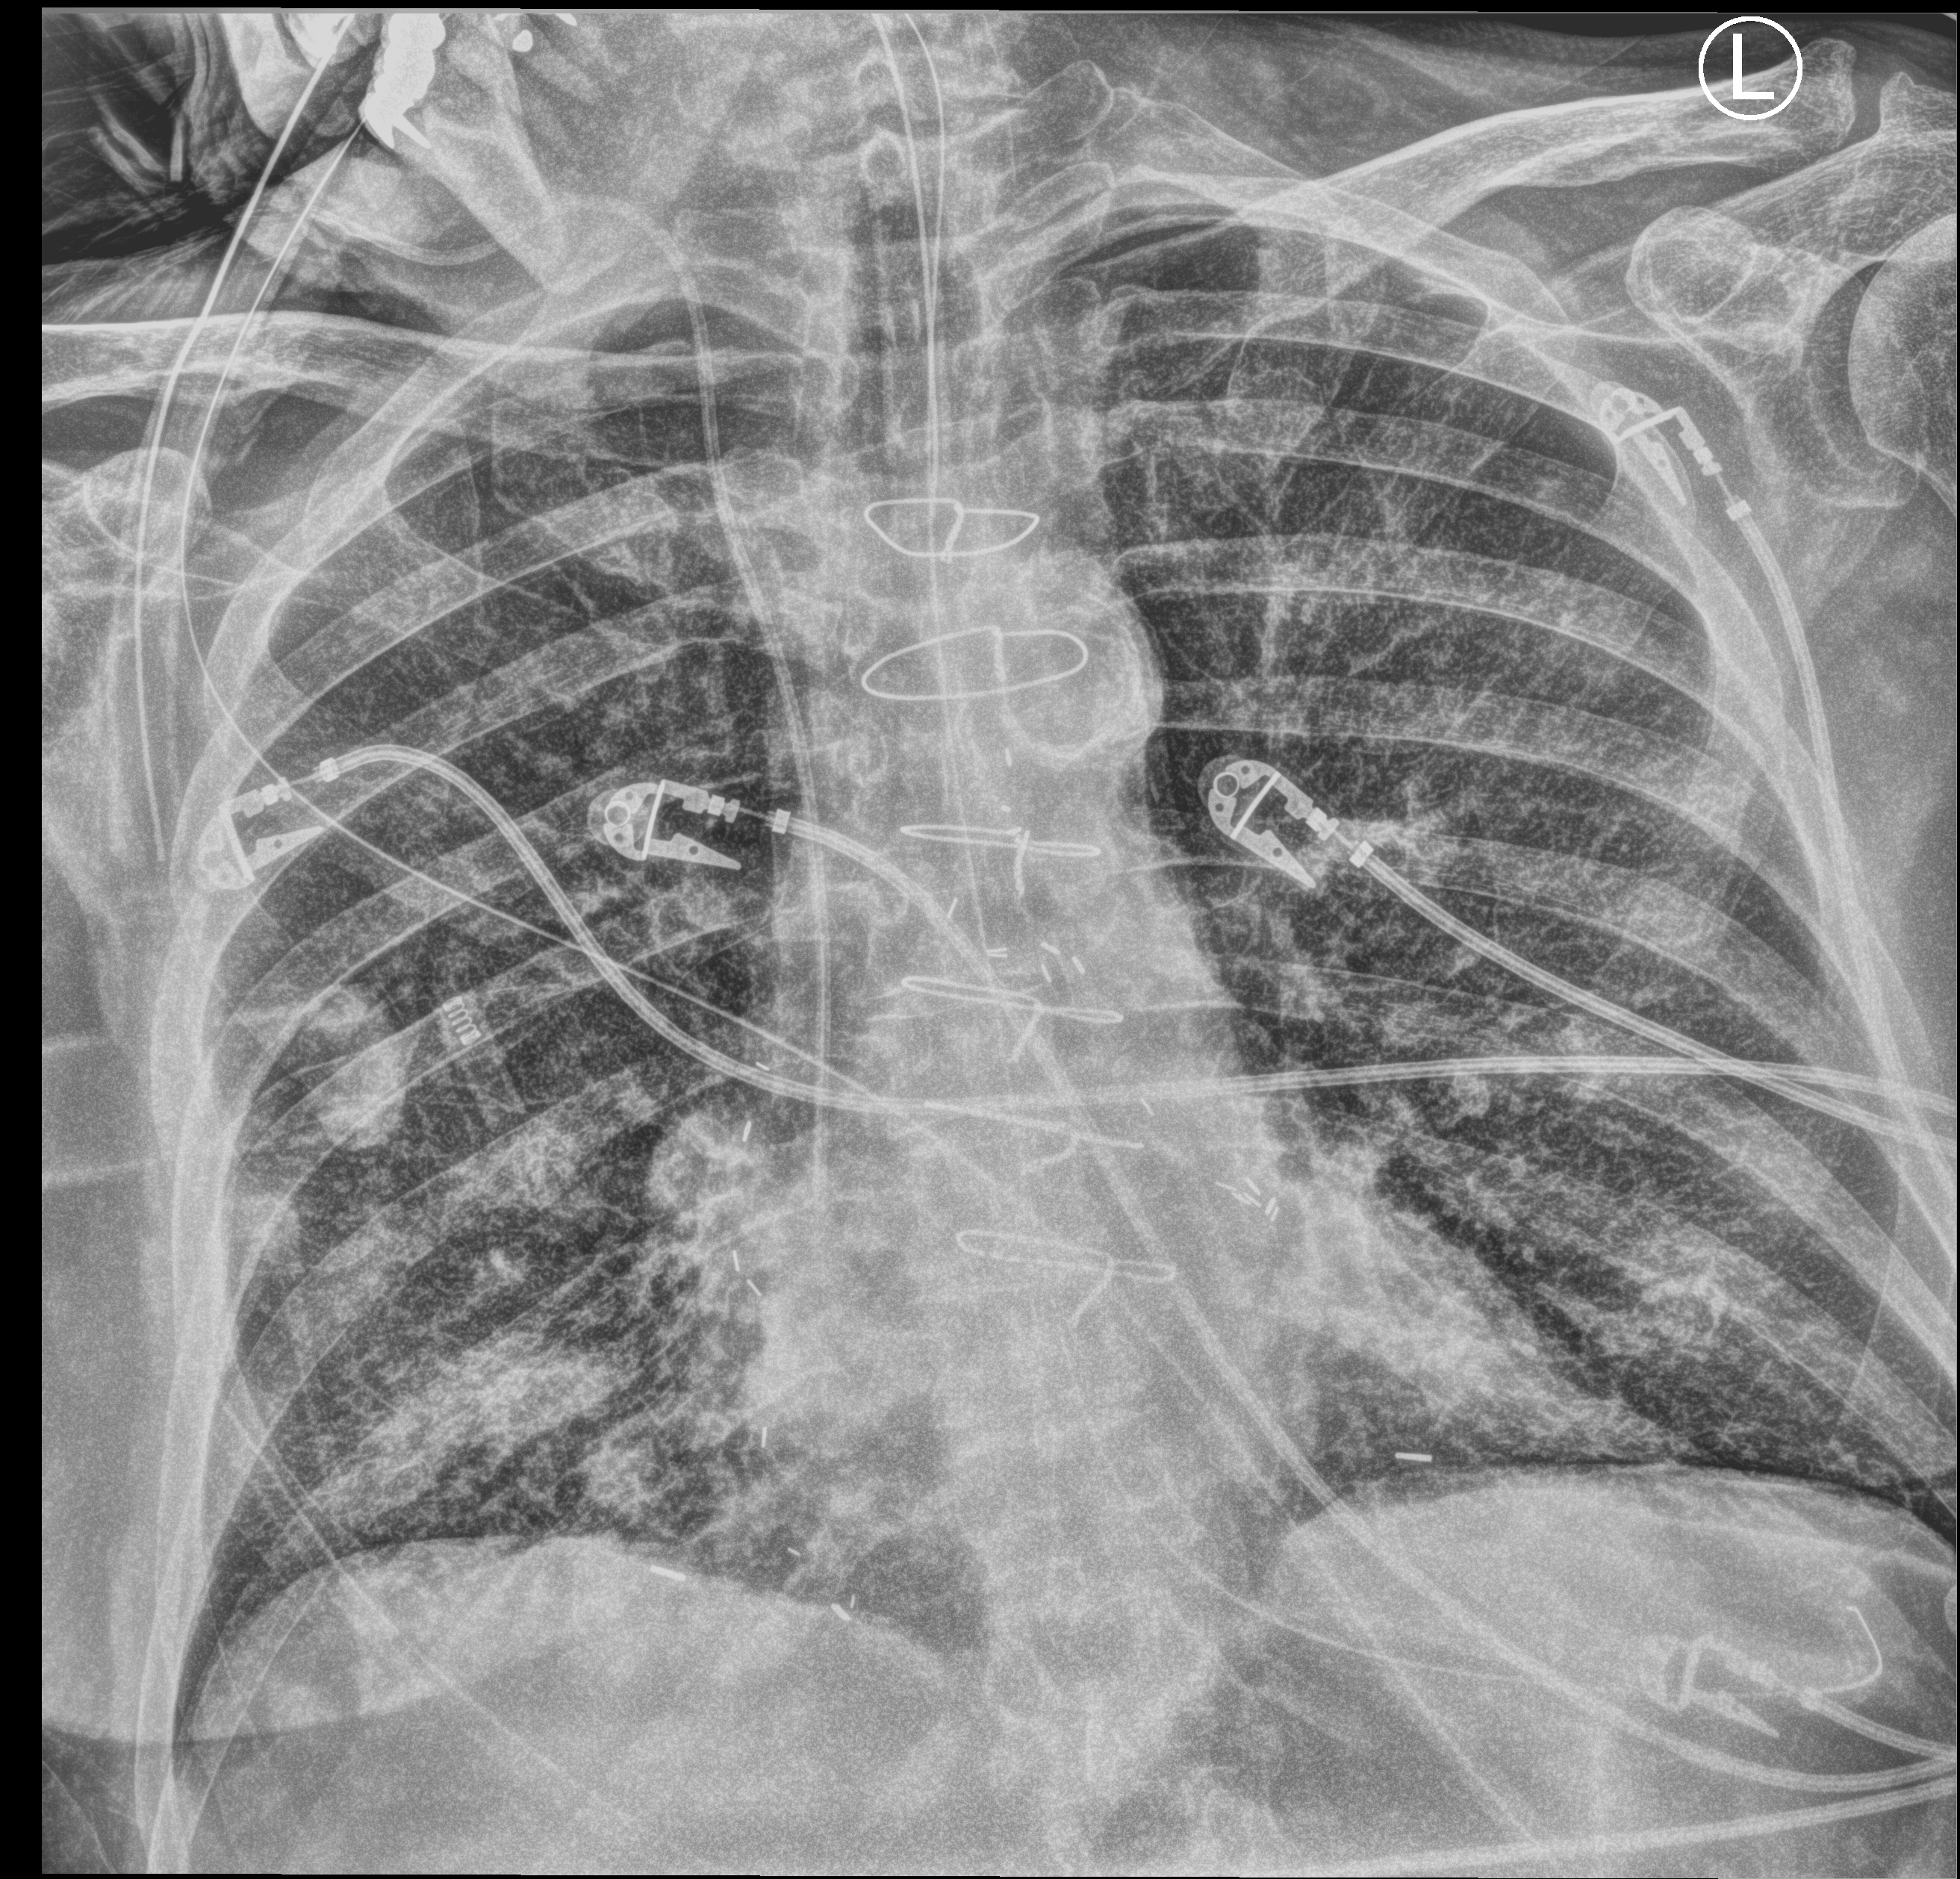
Chest X-ray (portable). Patient hospitalised with COVID-19; male, aged 75–90 years.
Admission-level facts for this patient (not findings on this image; timing relative to this image not recorded):
- mechanically ventilated during this hospital stay: yes